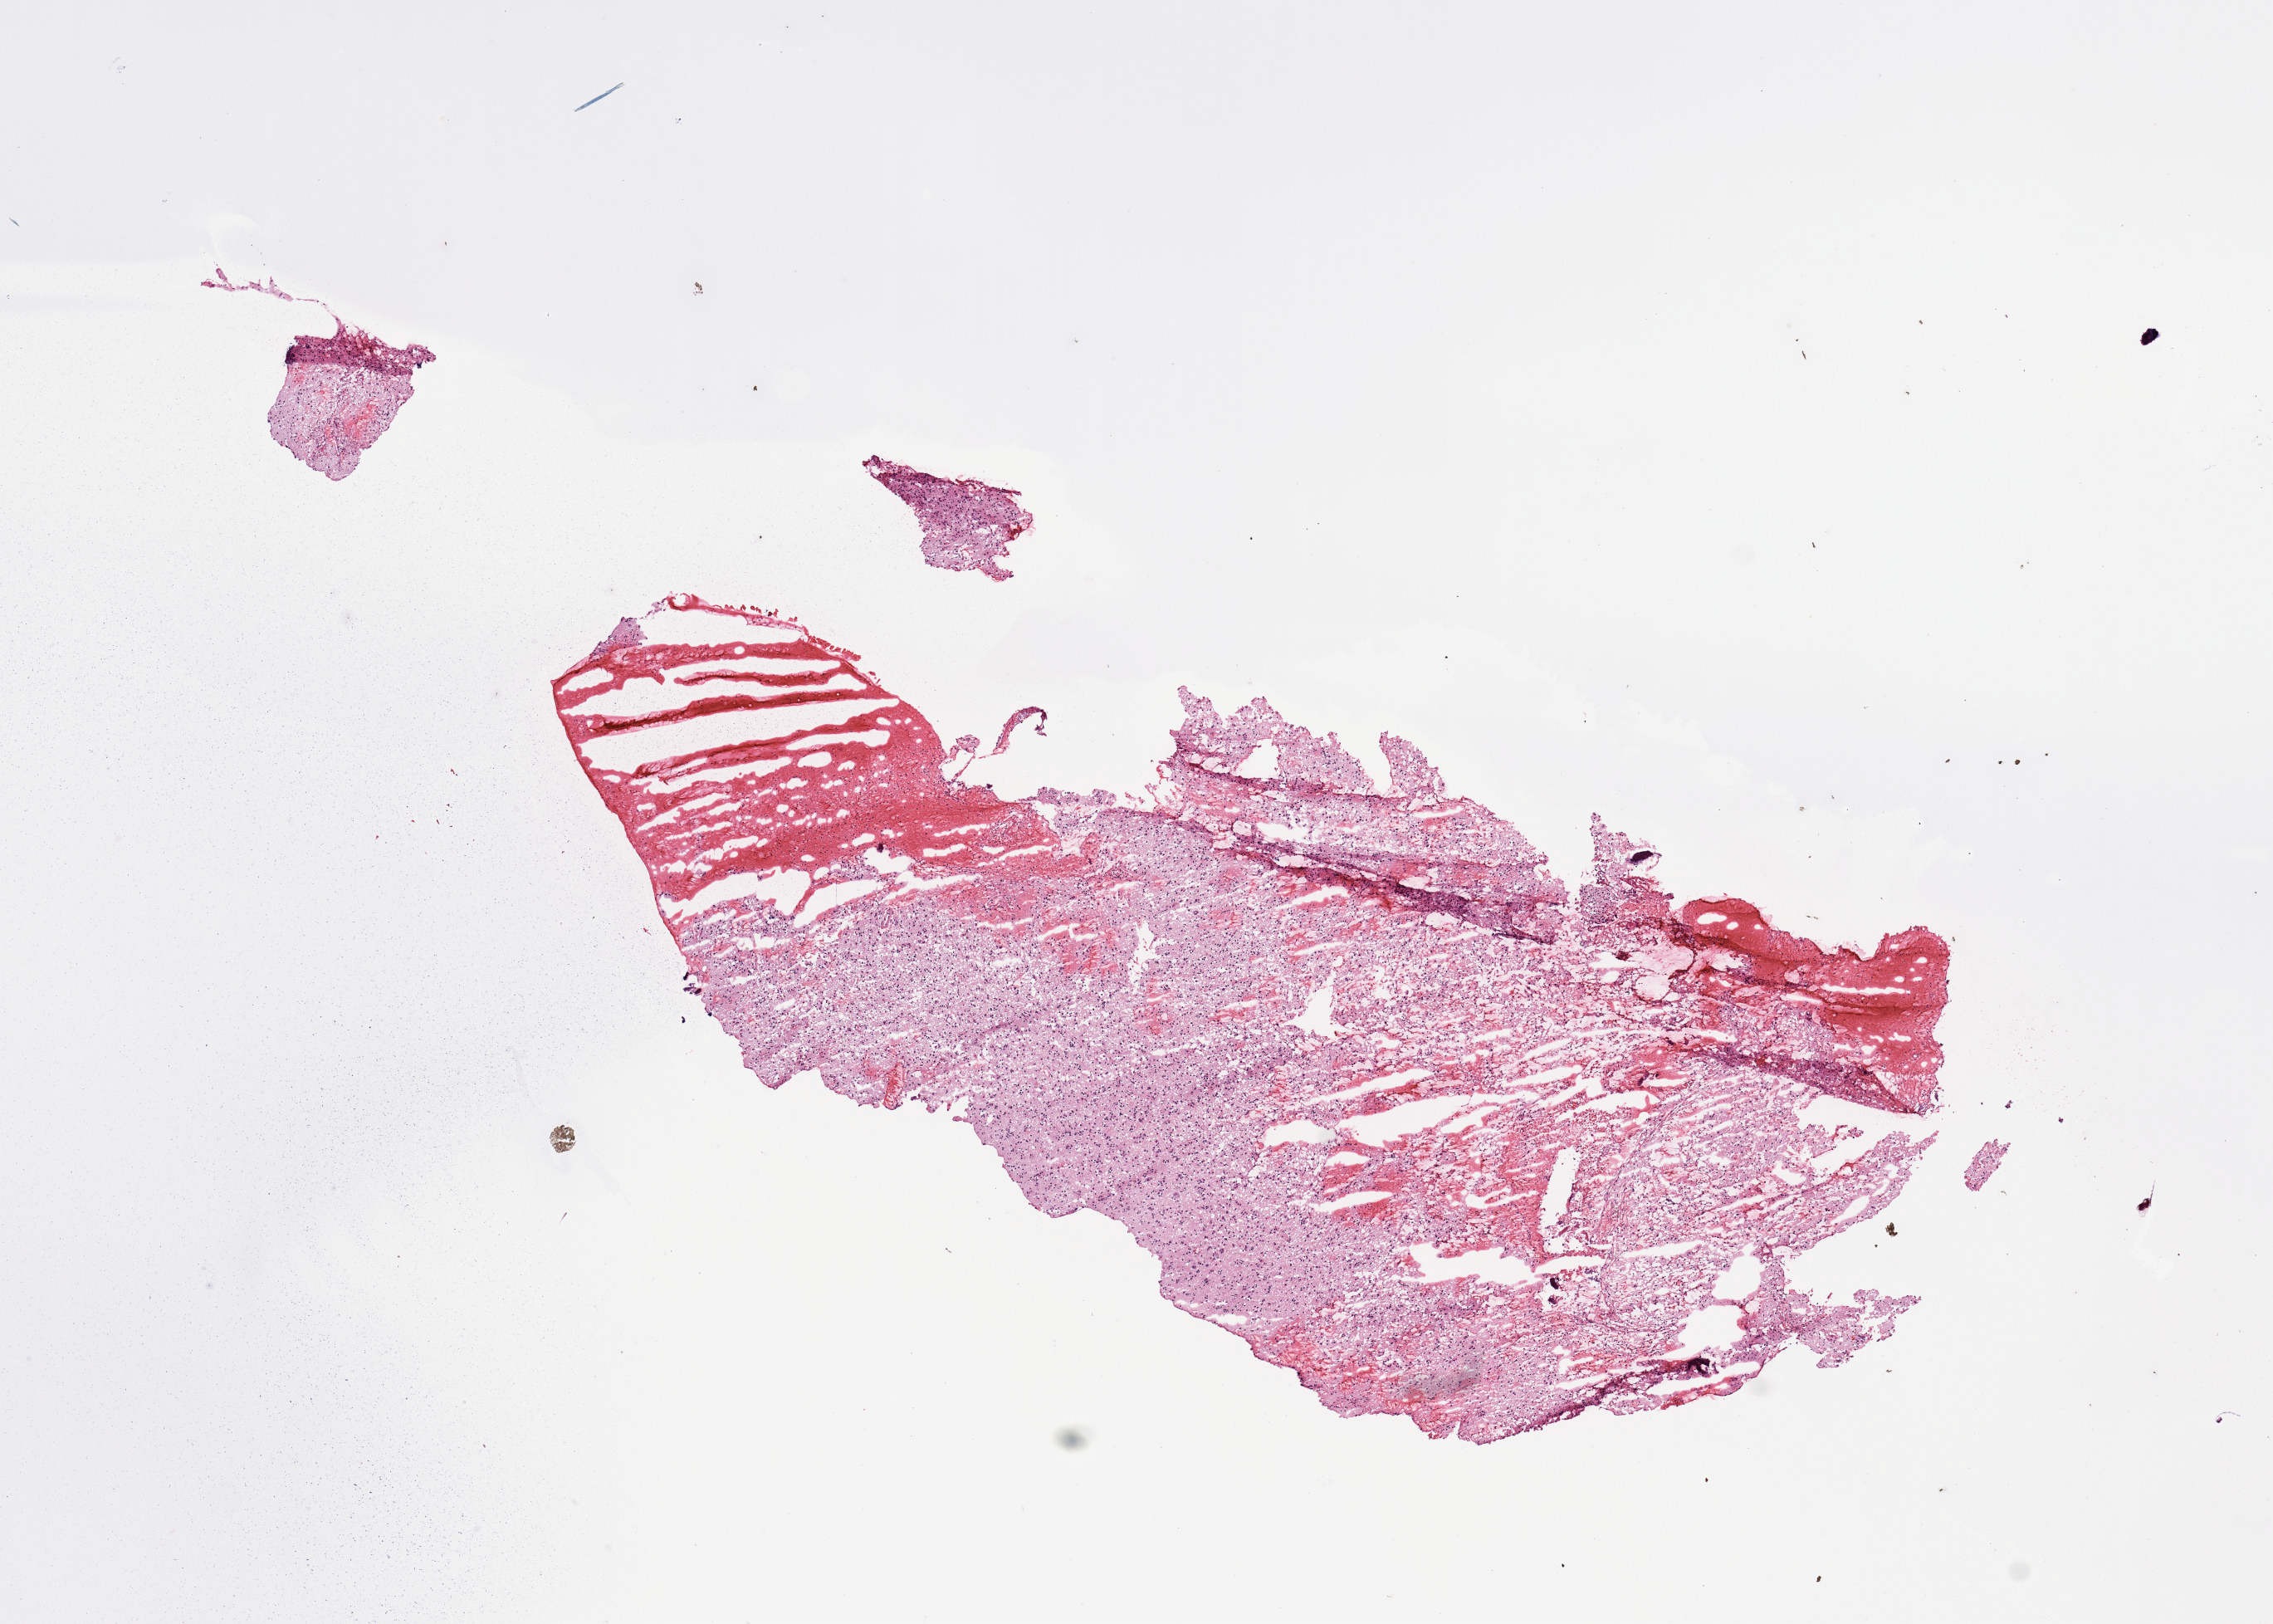
Whole-slide histology image, H&E — low-resolution overview of the scanned area, about 10.8 x 7.7 mm; tumour tissue sample, brain. Male, 51 y/o.
• primary tumour site (as recorded): frontal lobe
• patient diagnosis (cohort enrolment): glioblastoma multiforme (brain)